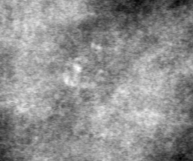
Region of interest cut from a scanned film mammogram (one marked finding), left breast, MLO view, BI-RADS breast density category 4 (scale 1–4).
Finding: calcifications, morphology pleomorphic, distribution clustered; BI-RADS assessment category 4; subtlety rating 1 on a 1 (subtle) to 5 (obvious) scale; pathology (as recorded): benign.